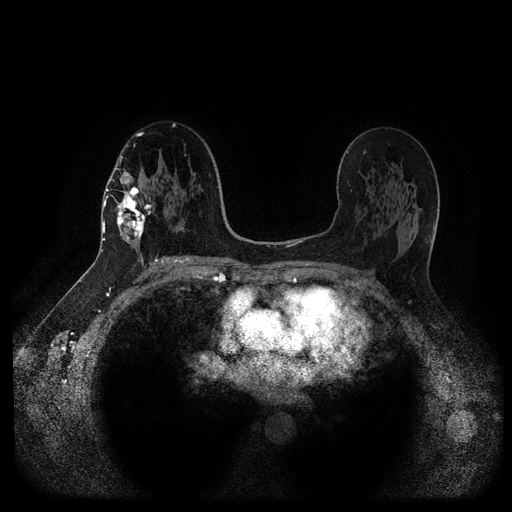
Breast MRI (dynamic contrast-enhanced, multi-phase), one axial slice; position 59 of 116 along the scan axis; dynamic contrast-enhanced series, time point 2 of 5 at this slice position (early post-contrast); 1.5 T; TE 2.6 ms, TR 5.3 ms; 2 mm slice thickness; 512 × 512 image matrix, field of view 360 × 360 mm. Female patient, age 58 years.
Structures marked on this image (semi-automatically segmented with operator editing):
- breast lesion (labelled 'tumour' in the annotation; benign lesions carry a separate 'benign' label): bounding box [x1, y1, x2, y2] px = [115, 185, 154, 241]